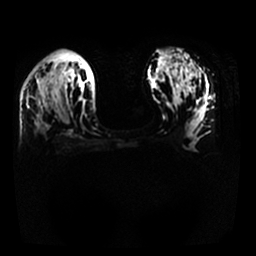
Breast MRI, one axial slice; slice 20 of 25 in the series (ordered by position); diffusion-weighted series; image 2 of 4 stored at this slice position (different b-values; order by instance number); 1.5 T; 4 mm slice thickness; 256 × 256 image matrix, field of view 340 × 340 mm. Female patient.
Outlined on this slice (outlined manually by an expert reader):
- tumour on diffusion-weighted imaging: bounding box <38,127,45,132> (left, top, right, bottom; pixels)